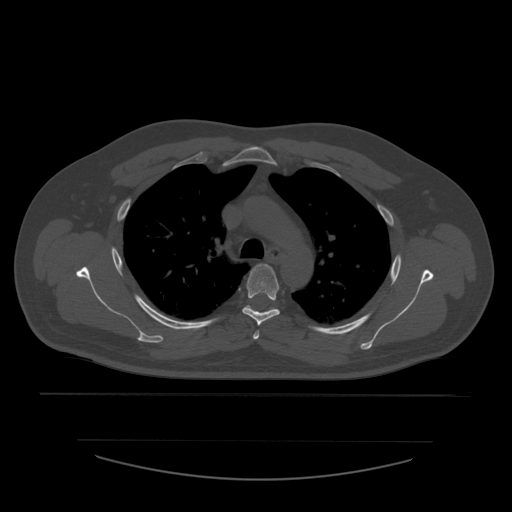
CT including the spine, one axial slice; slice 416 of 532 in the series (ordered by position); reconstruction kernel STANDARD; bone window (W 1800 / L 400 HU); 512 × 512 image matrix, field of view 441 × 441 mm. Patient age 44 years. From the clinical record (not read from this slice): primary cancer: soft tissue sarcoma.
Outlined on this slice (semi-automatic segmentation, software-assisted and operator-edited):
- T3 vertebra: bounding box (x1, y1, x2, y2) in pixels: (253, 325, 260, 340)
- T4 vertebra: (242, 264, 280, 325)
- T5 vertebra: (246, 306, 277, 312)